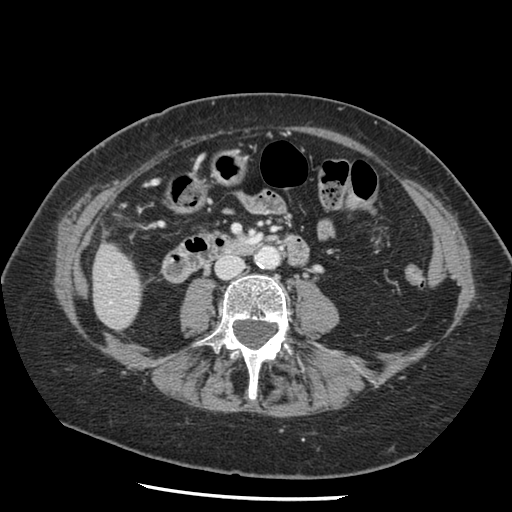
Contrast-enhanced abdominal CT, one axial slice. Position 25 of 148 along the scan axis. 120 kVp. Intravenous contrast given. Soft-tissue window (W 400 / L 40 HU). 512 × 512 image matrix, field of view 330 × 330 mm. Female patient, age 85 years. From the clinical record (not read from this slice): diagnosis: colorectal cancer liver metastases, imaged before liver resection; multiple liver metastases: no; largest metastasis: 0.9 cm; disease in both lobes: no.
Structures marked on this image (outlined manually by an expert reader):
- liver: bounding box [x1, y1, x2, y2] px = [94, 245, 142, 329]
- planned liver remnant (the part of the liver to remain after resection): [94, 245, 142, 329]